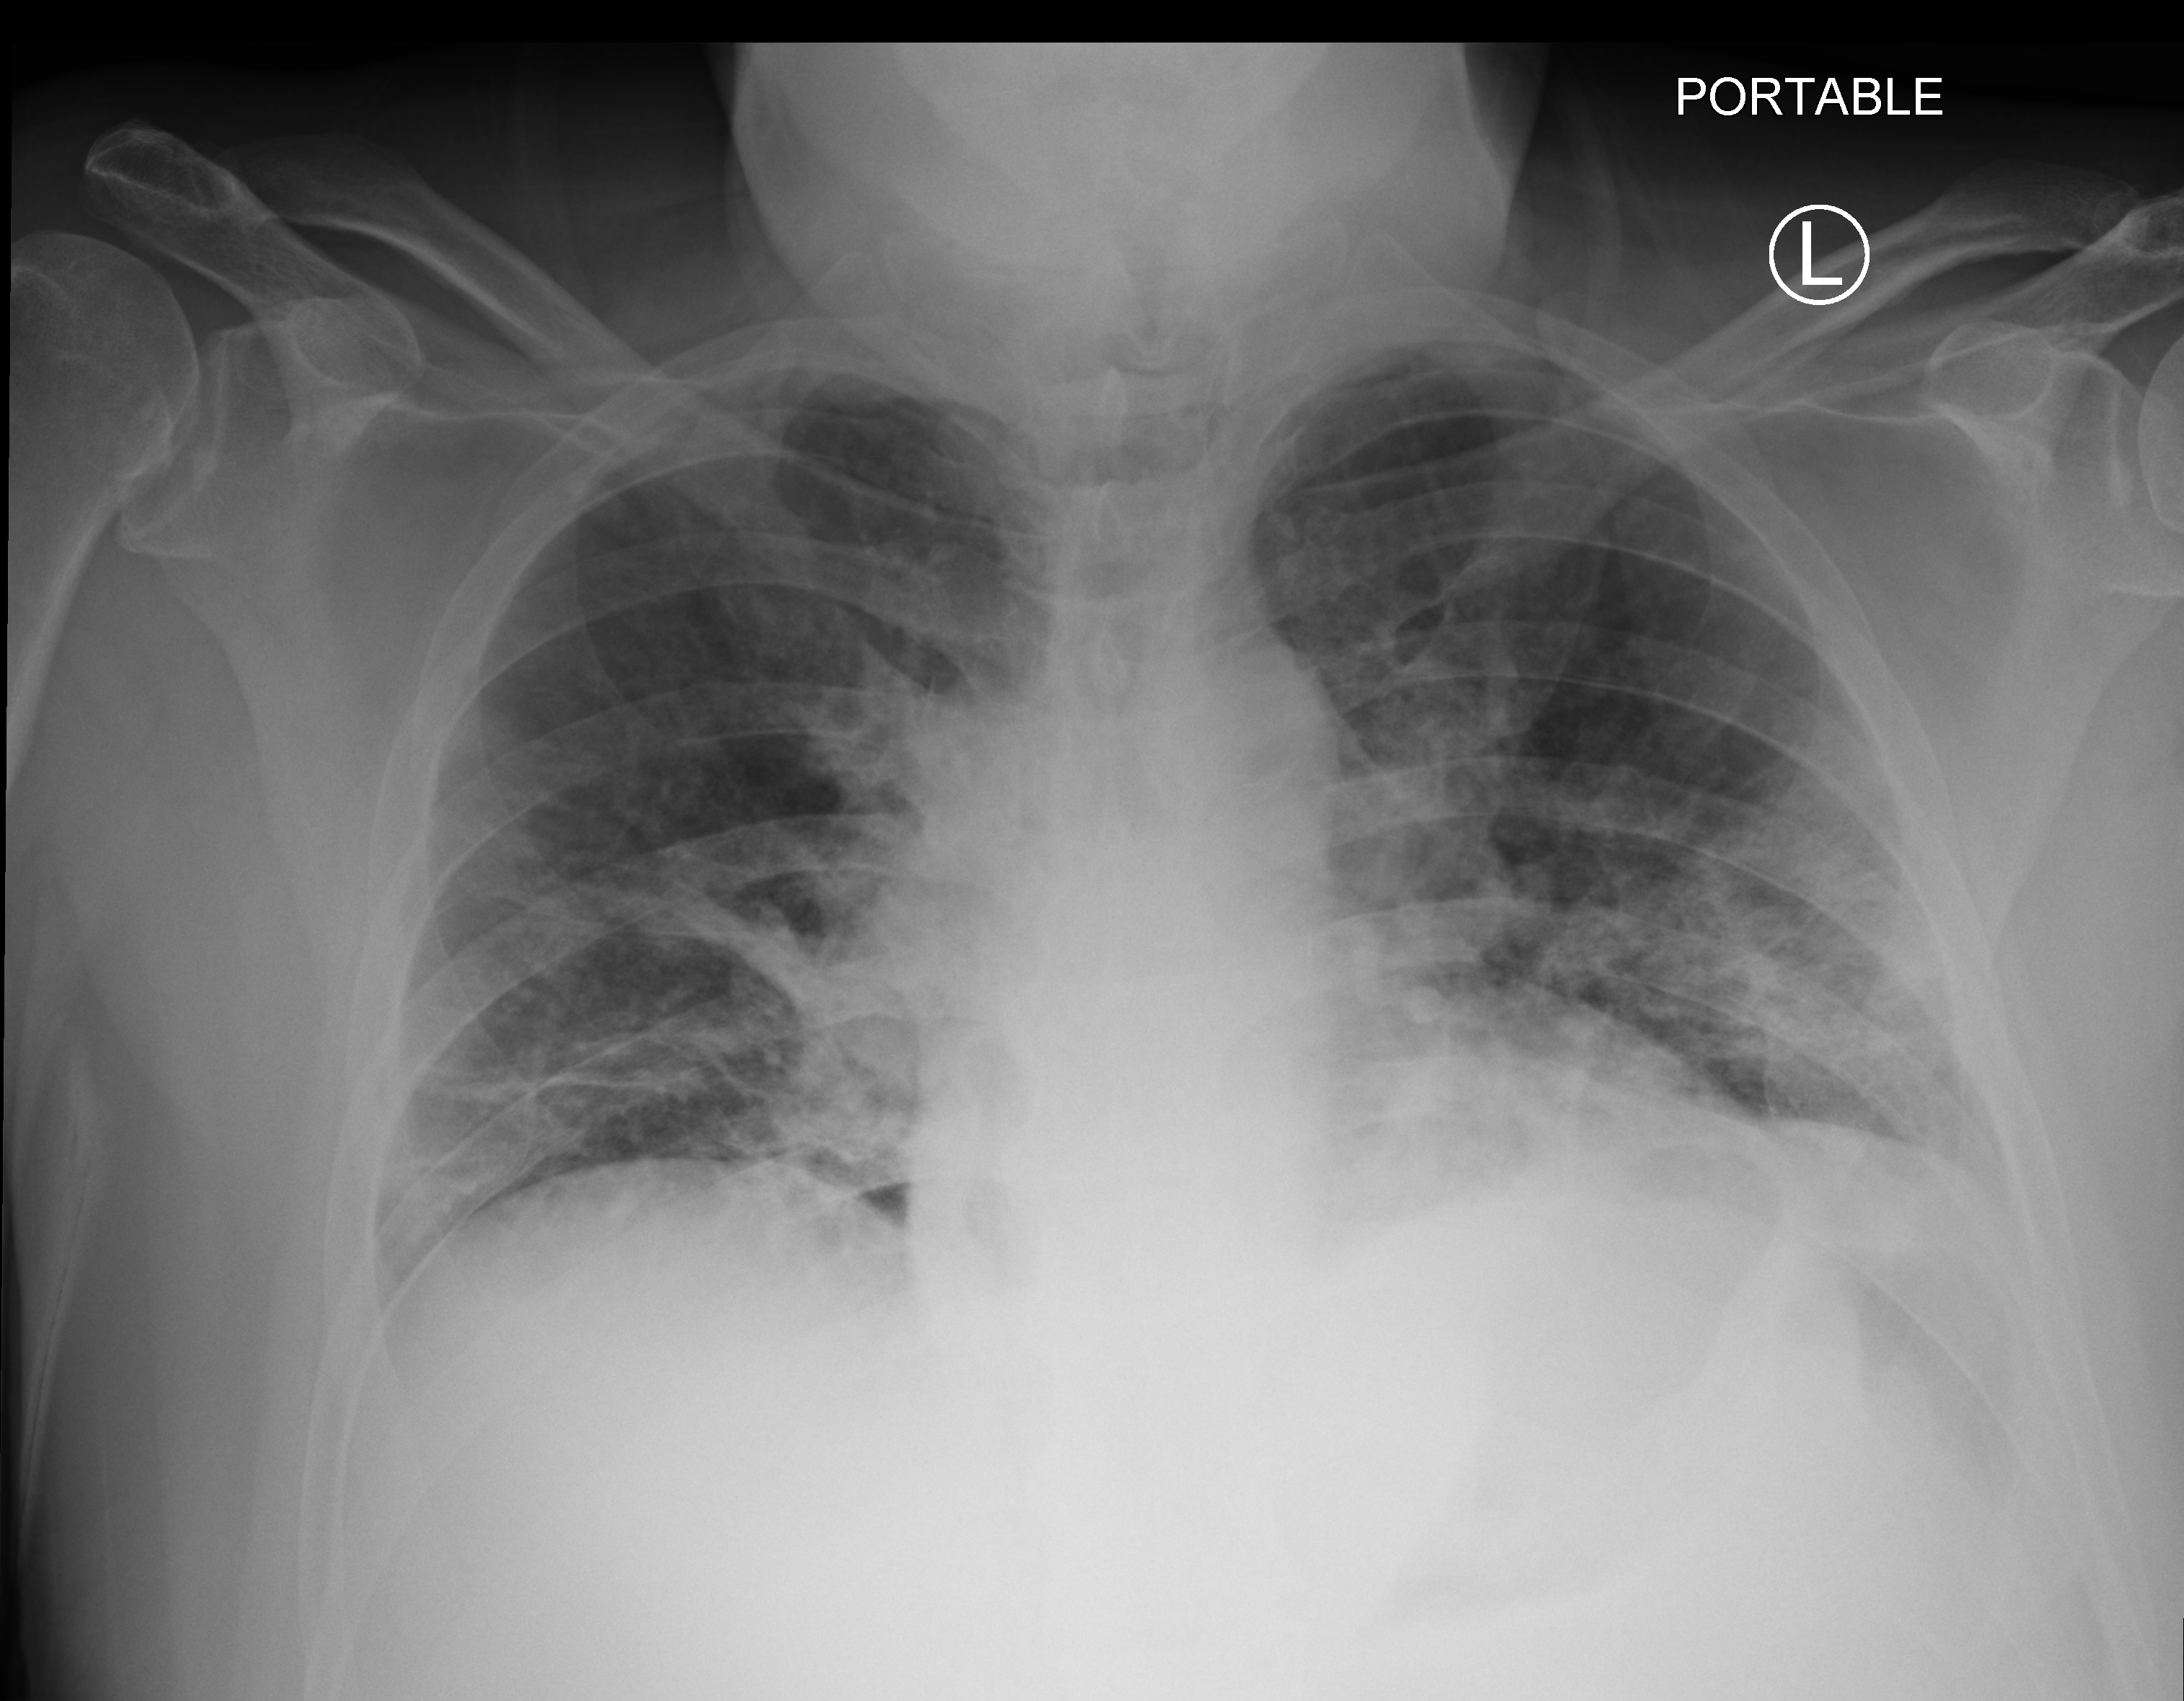
Chest X-ray (portable). Male patient hospitalised with COVID-19, age 60–74 years.
From the hospital-stay record, not from the radiograph (when in the stay this image was taken is not recorded): length of hospital stay: 14 days.